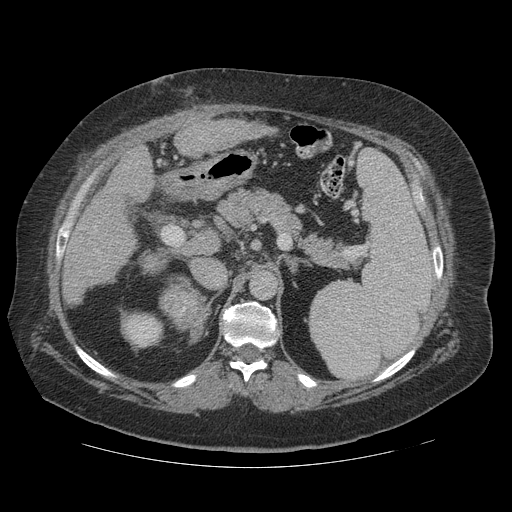
Contrast-enhanced abdominal CT (liver protocol), one axial slice. Position 66 of 121 along the scan axis. Reconstruction kernel STANDARD. Soft-tissue window (W 400 / L 40 HU). 512 × 512 image matrix, field of view 420 × 420 mm. From the clinical record (not read from this slice): diagnosis: hepatocellular carcinoma (patient treated with transarterial chemoembolisation; whether this scan precedes or follows treatment is not stated here); TNM stage (as recorded): Stage-IIIA.
Annotated regions visible in this slice (semi-automatically segmented with operator editing):
- liver parenchyma outside the tumour (the mass and vessels are separate outlines, so this box may not span the whole liver): bounding box [x1, y1, x2, y2] px = [71, 120, 275, 256]
- mass: [161, 283, 210, 336]
- liver vessels: [94, 137, 202, 229]